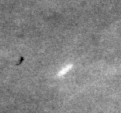
Region of interest cut from a scanned film mammogram (one marked finding), right breast, MLO view.
Calcifications, distribution regional; BI-RADS assessment category 2; benign without callback (not worked up further).